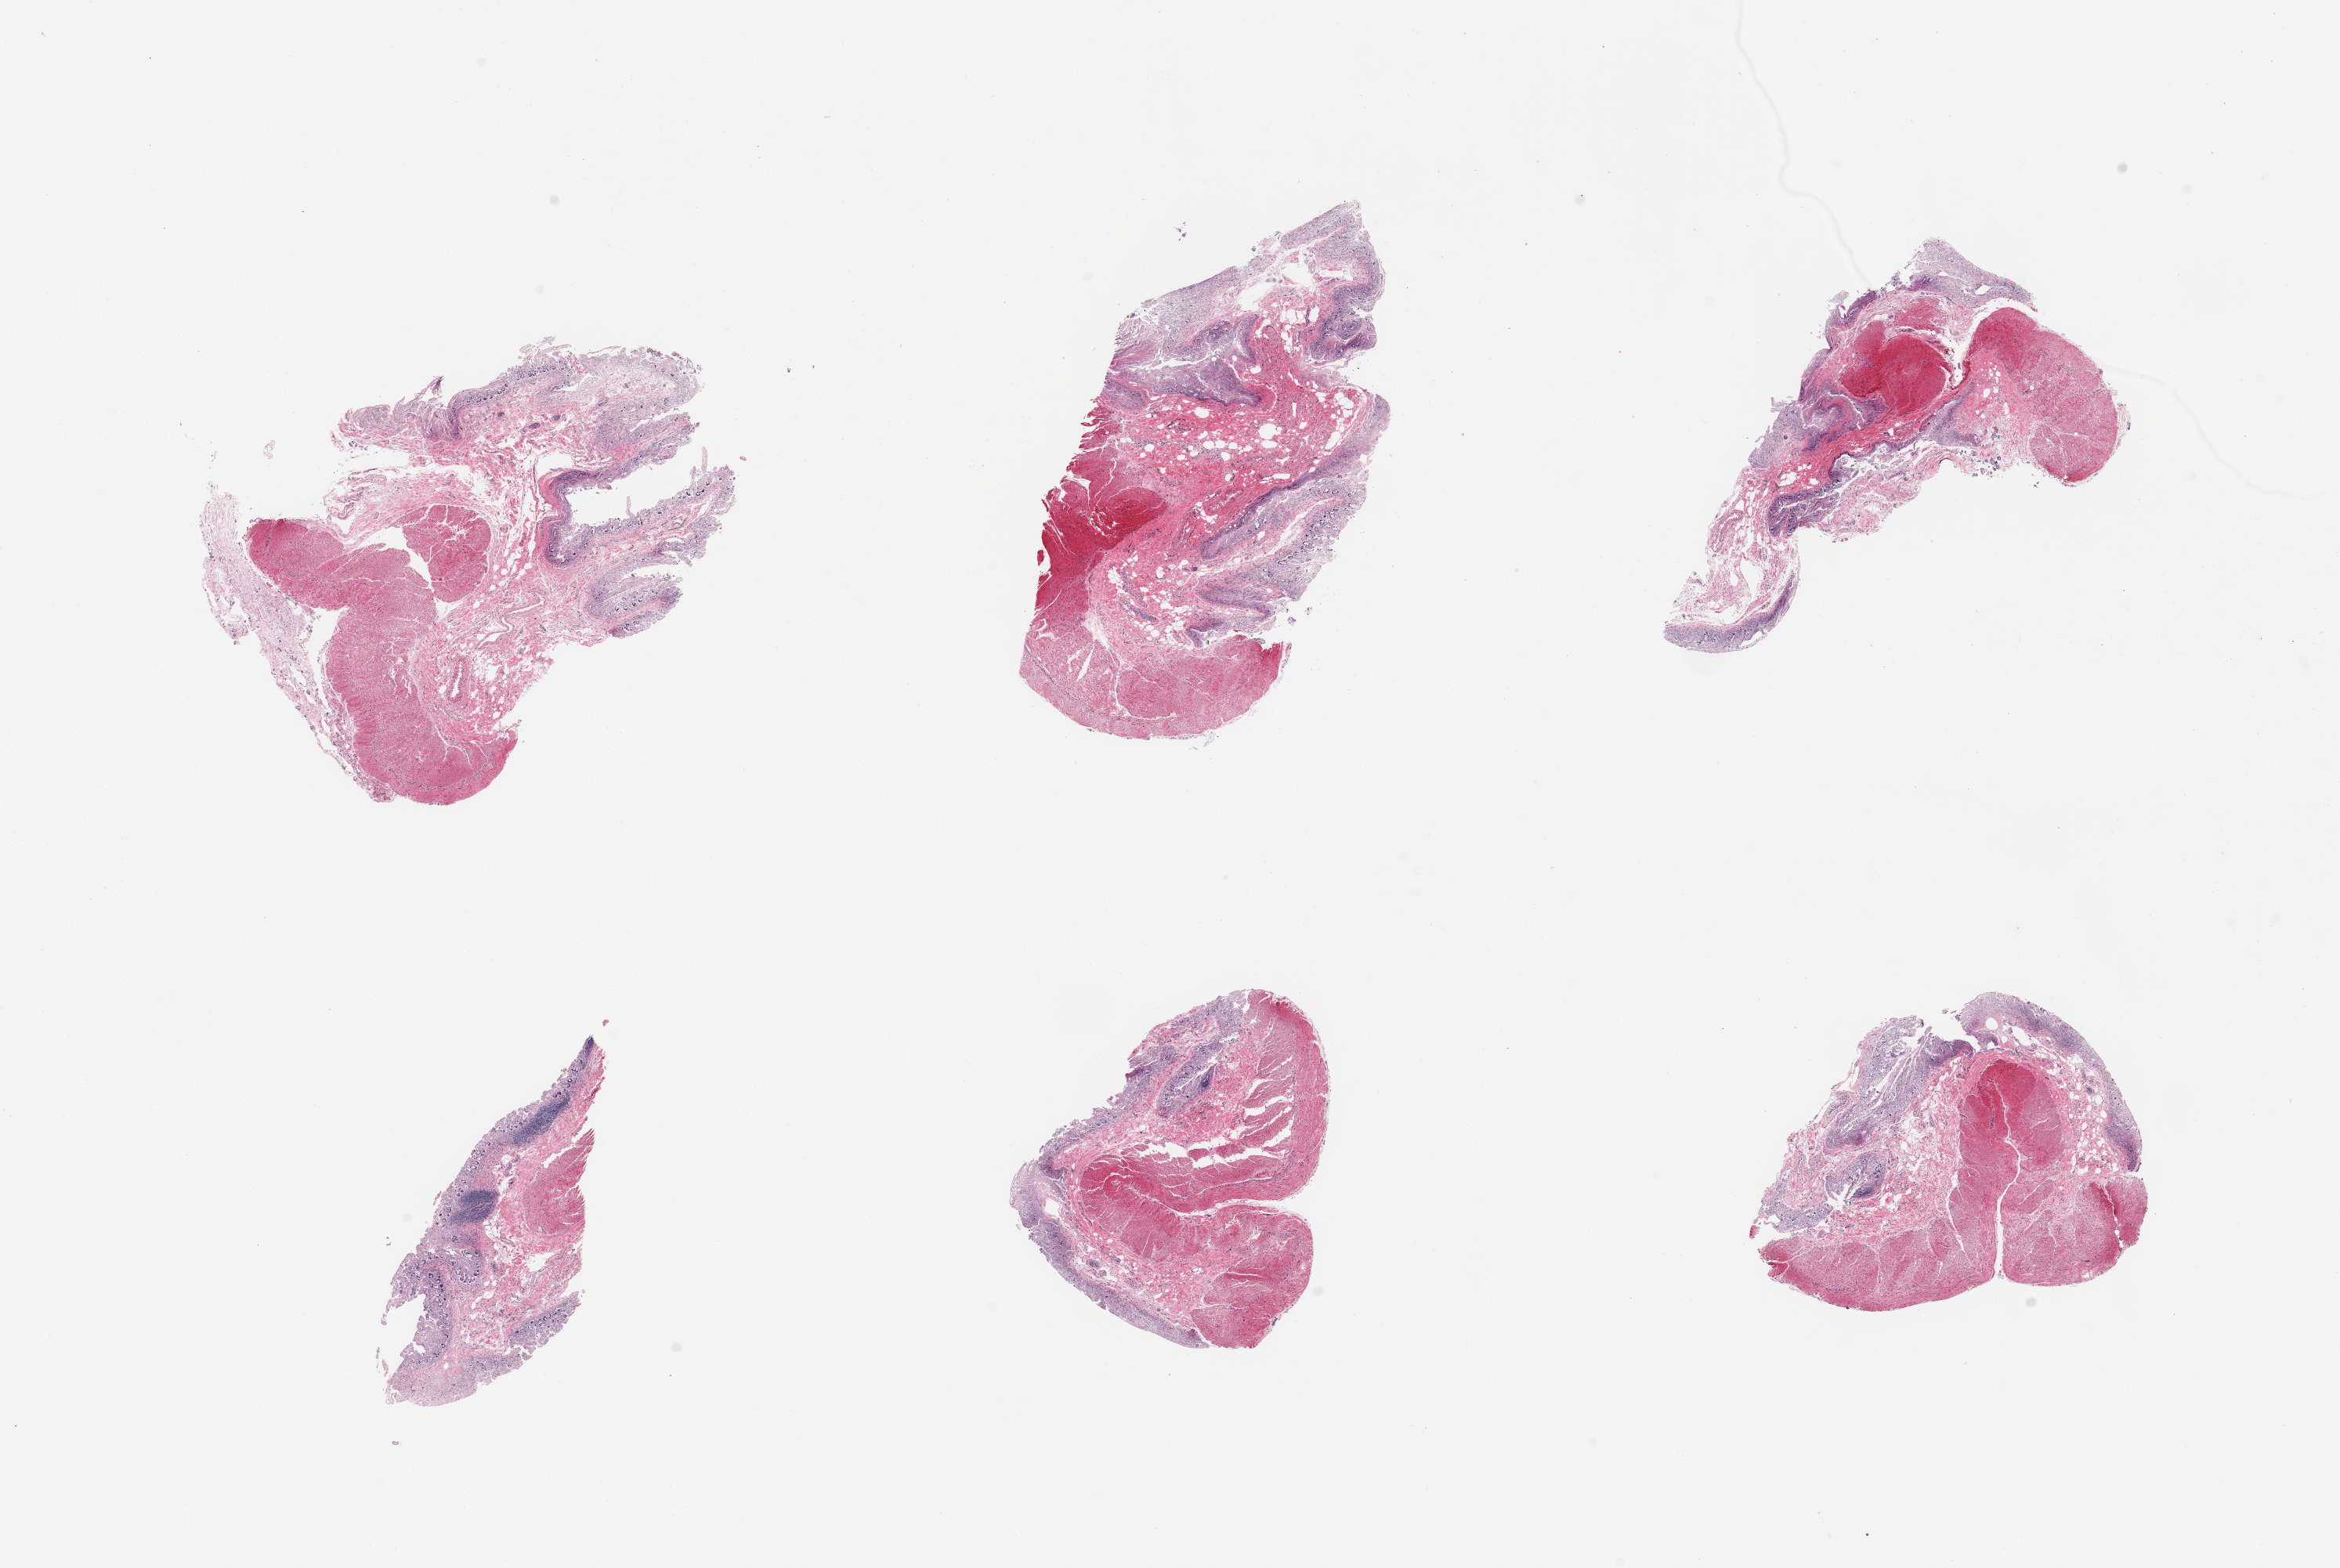
H&E whole-slide image, brightfield — low-resolution overview of the scanned area, about 23.6 x 15.8 mm (acquisition: 20x scan), PAXgene-fixed paraffin-embedded (PFPE) section, section of transverse colon (target tissue), tissue donor sample. Donor sex: male.
Review note (as recorded): 6 pieces; autolyzed mucosa (3) and muscularis (2).